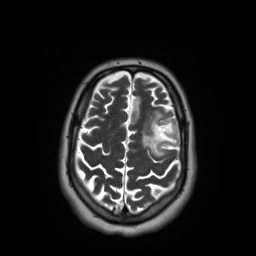
Brain MRI from a brain-tumour surgery series, one axial slice. 3.03 mm slice thickness. 256 × 256 image matrix, field of view 250 × 250 mm. From the clinical record (not read from this slice): histopathology: Oligodendroglioma; WHO grade: 2; IDH mutation: yes.
Annotated regions visible in this slice (outlined manually by an expert reader):
- tumour: box from (x=139, y=109) to (x=180, y=156) px